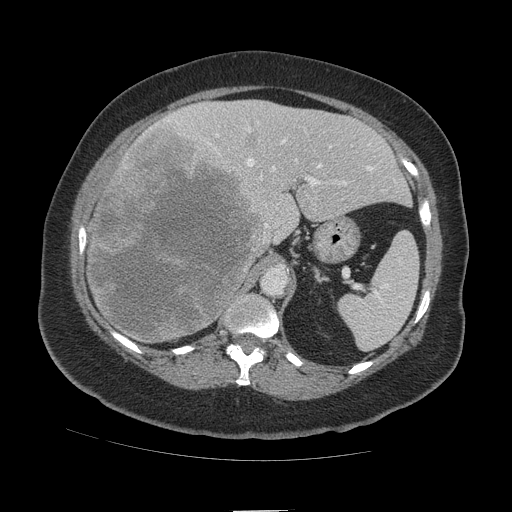
Contrast-enhanced abdominal CT (liver protocol), one axial slice; position 70 of 109 along the scan axis; reconstruction kernel STANDARD; 140 kVp; soft-tissue window (W 400 / L 40 HU); 512 × 512 image matrix. Case-level facts recorded for this patient, not image findings: diagnosis: hepatocellular carcinoma (patient treated with transarterial chemoembolisation; whether this scan precedes or follows treatment is not stated here); TNM stage (as recorded): Stage-IVB; Child-Pugh class: A; tumour differentiation: poorly differentiated; tumour nodularity: multinodular.
Structures marked on this image (semi-automatic segmentation, software-assisted and operator-edited):
- liver parenchyma outside the tumour (the mass and vessels are separate outlines, so this box may not span the whole liver): box from (x=88, y=100) to (x=410, y=338) px
- mass: (x=88, y=120)–(x=268, y=346)
- liver vessels: (x=168, y=110)–(x=395, y=186)